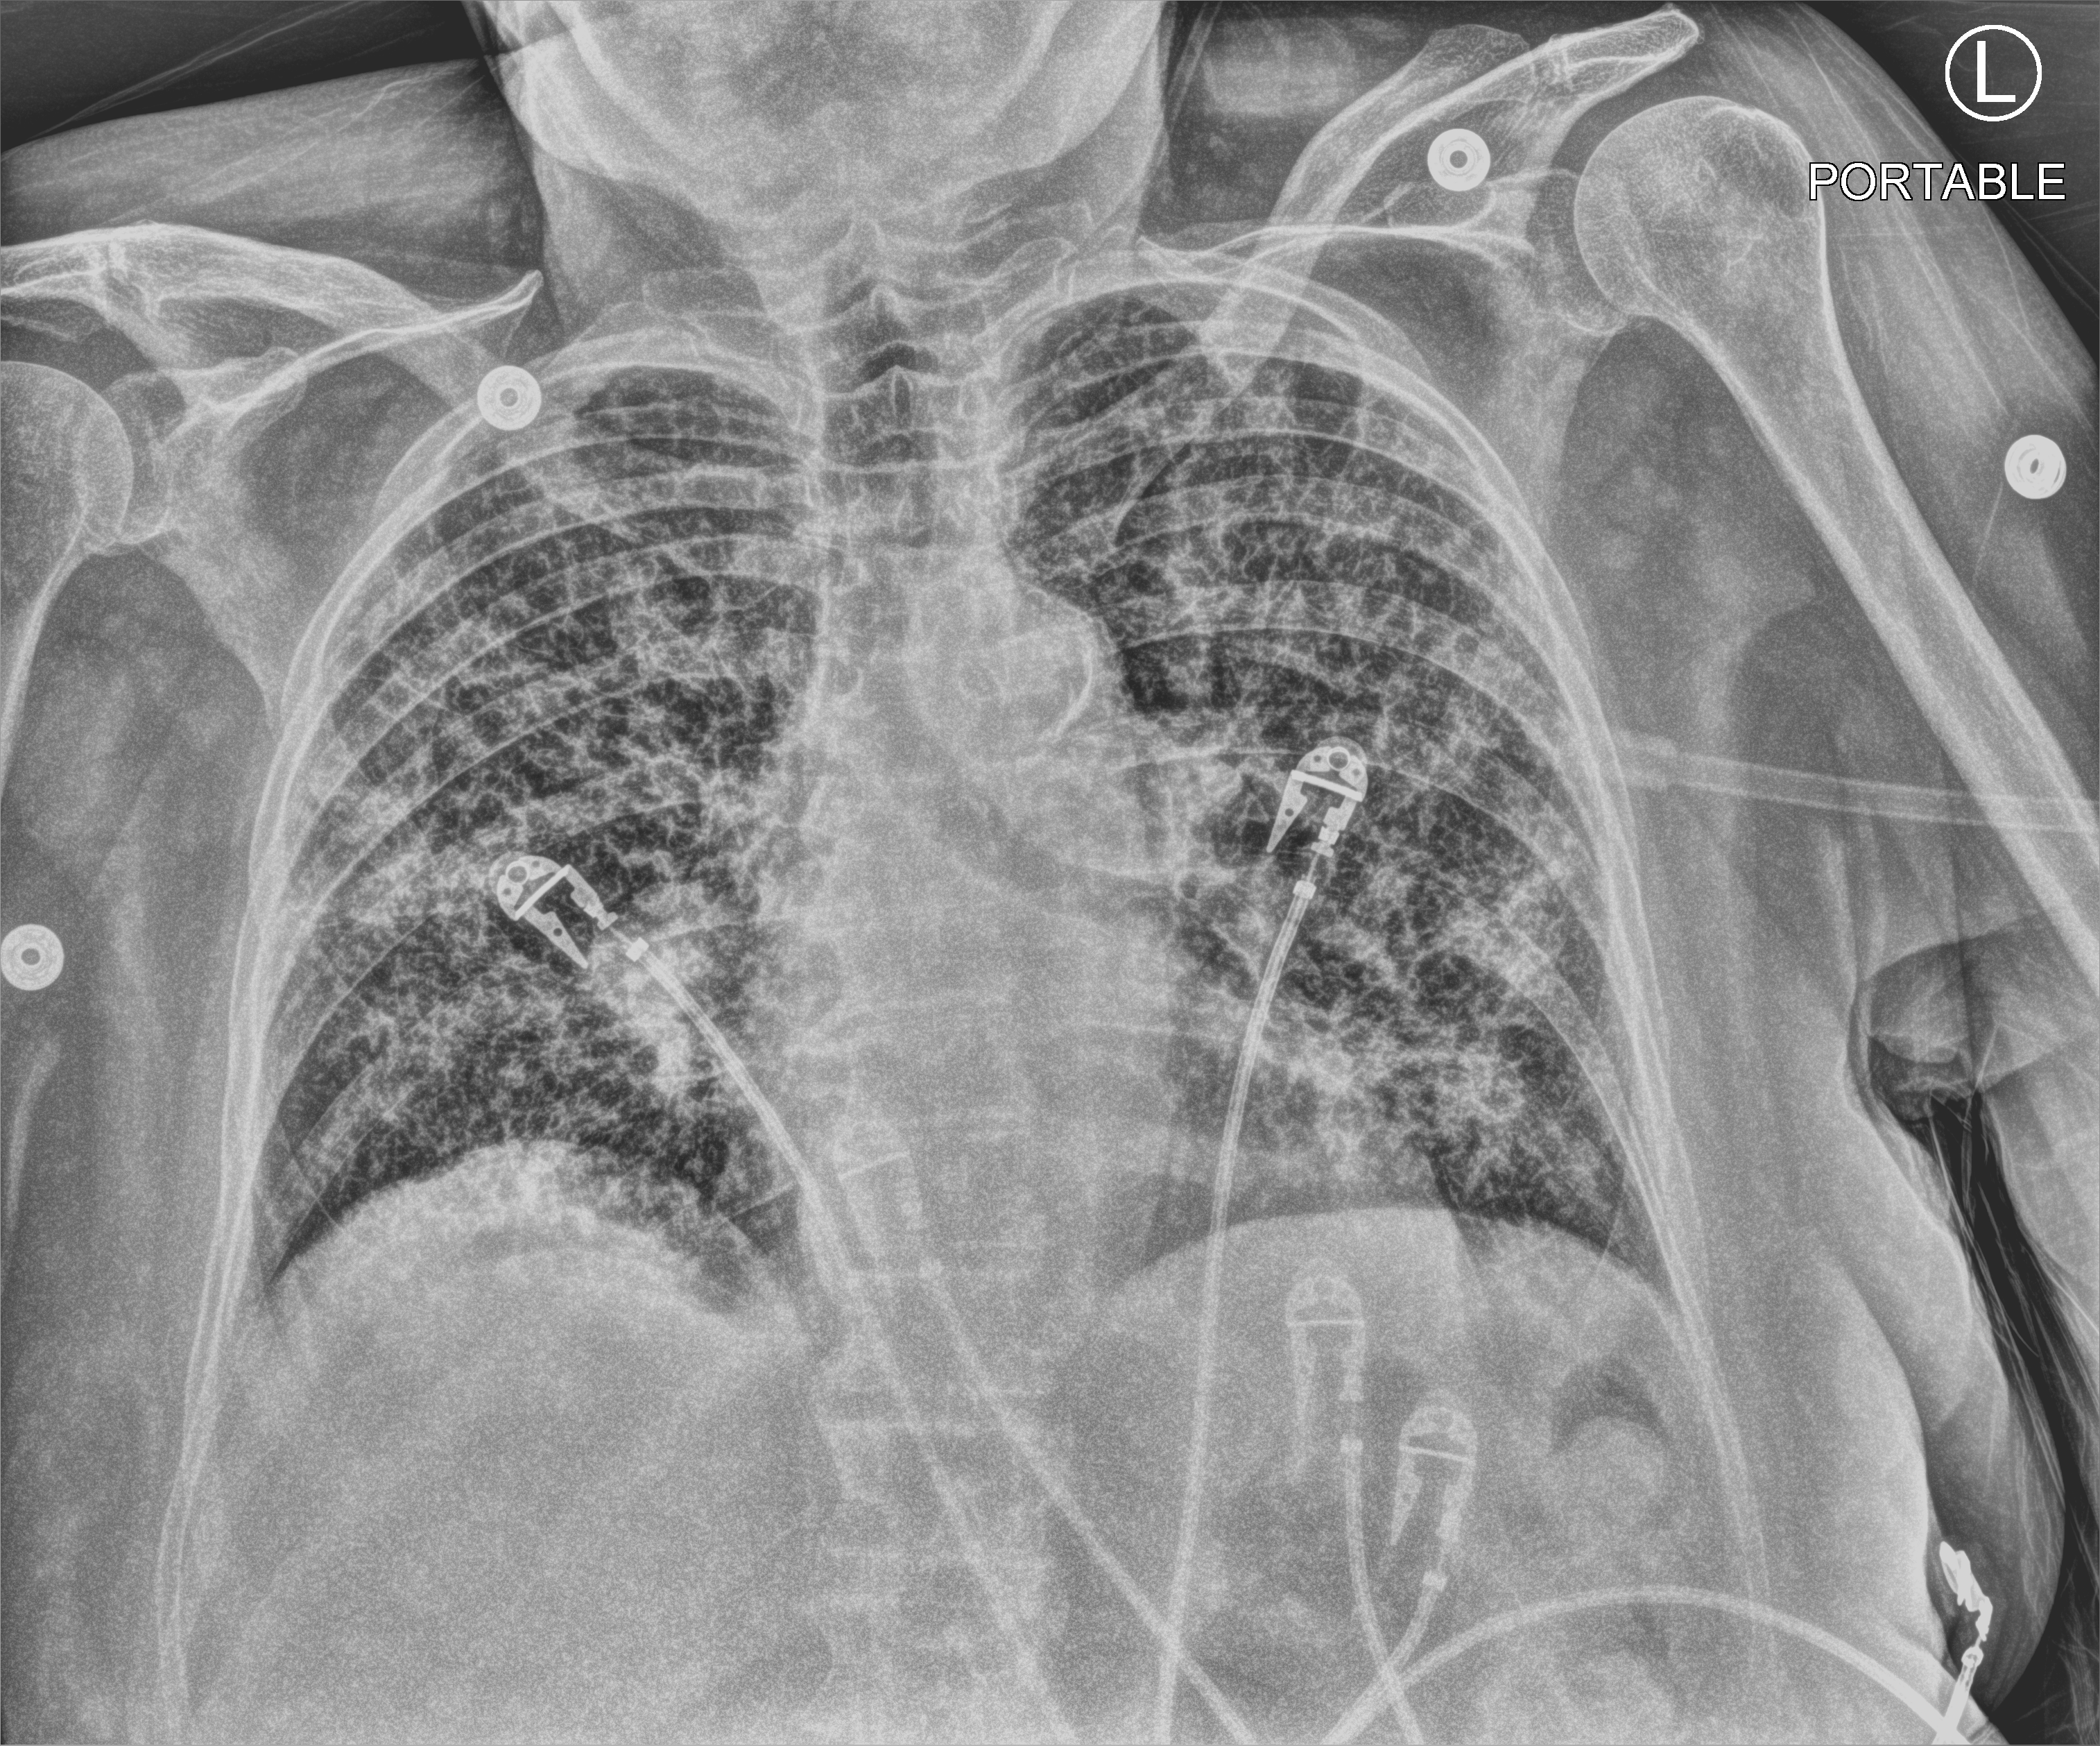
Bedside chest radiograph (computed radiography); anteroposterior (AP) projection. Patient hospitalised with COVID-19; female, aged 75–90 years.
Hospital-stay facts (about this admission, not read from this image; timing relative to this image not recorded): mechanically ventilated during this hospital stay: no; admitted to intensive care during this hospital stay: no.